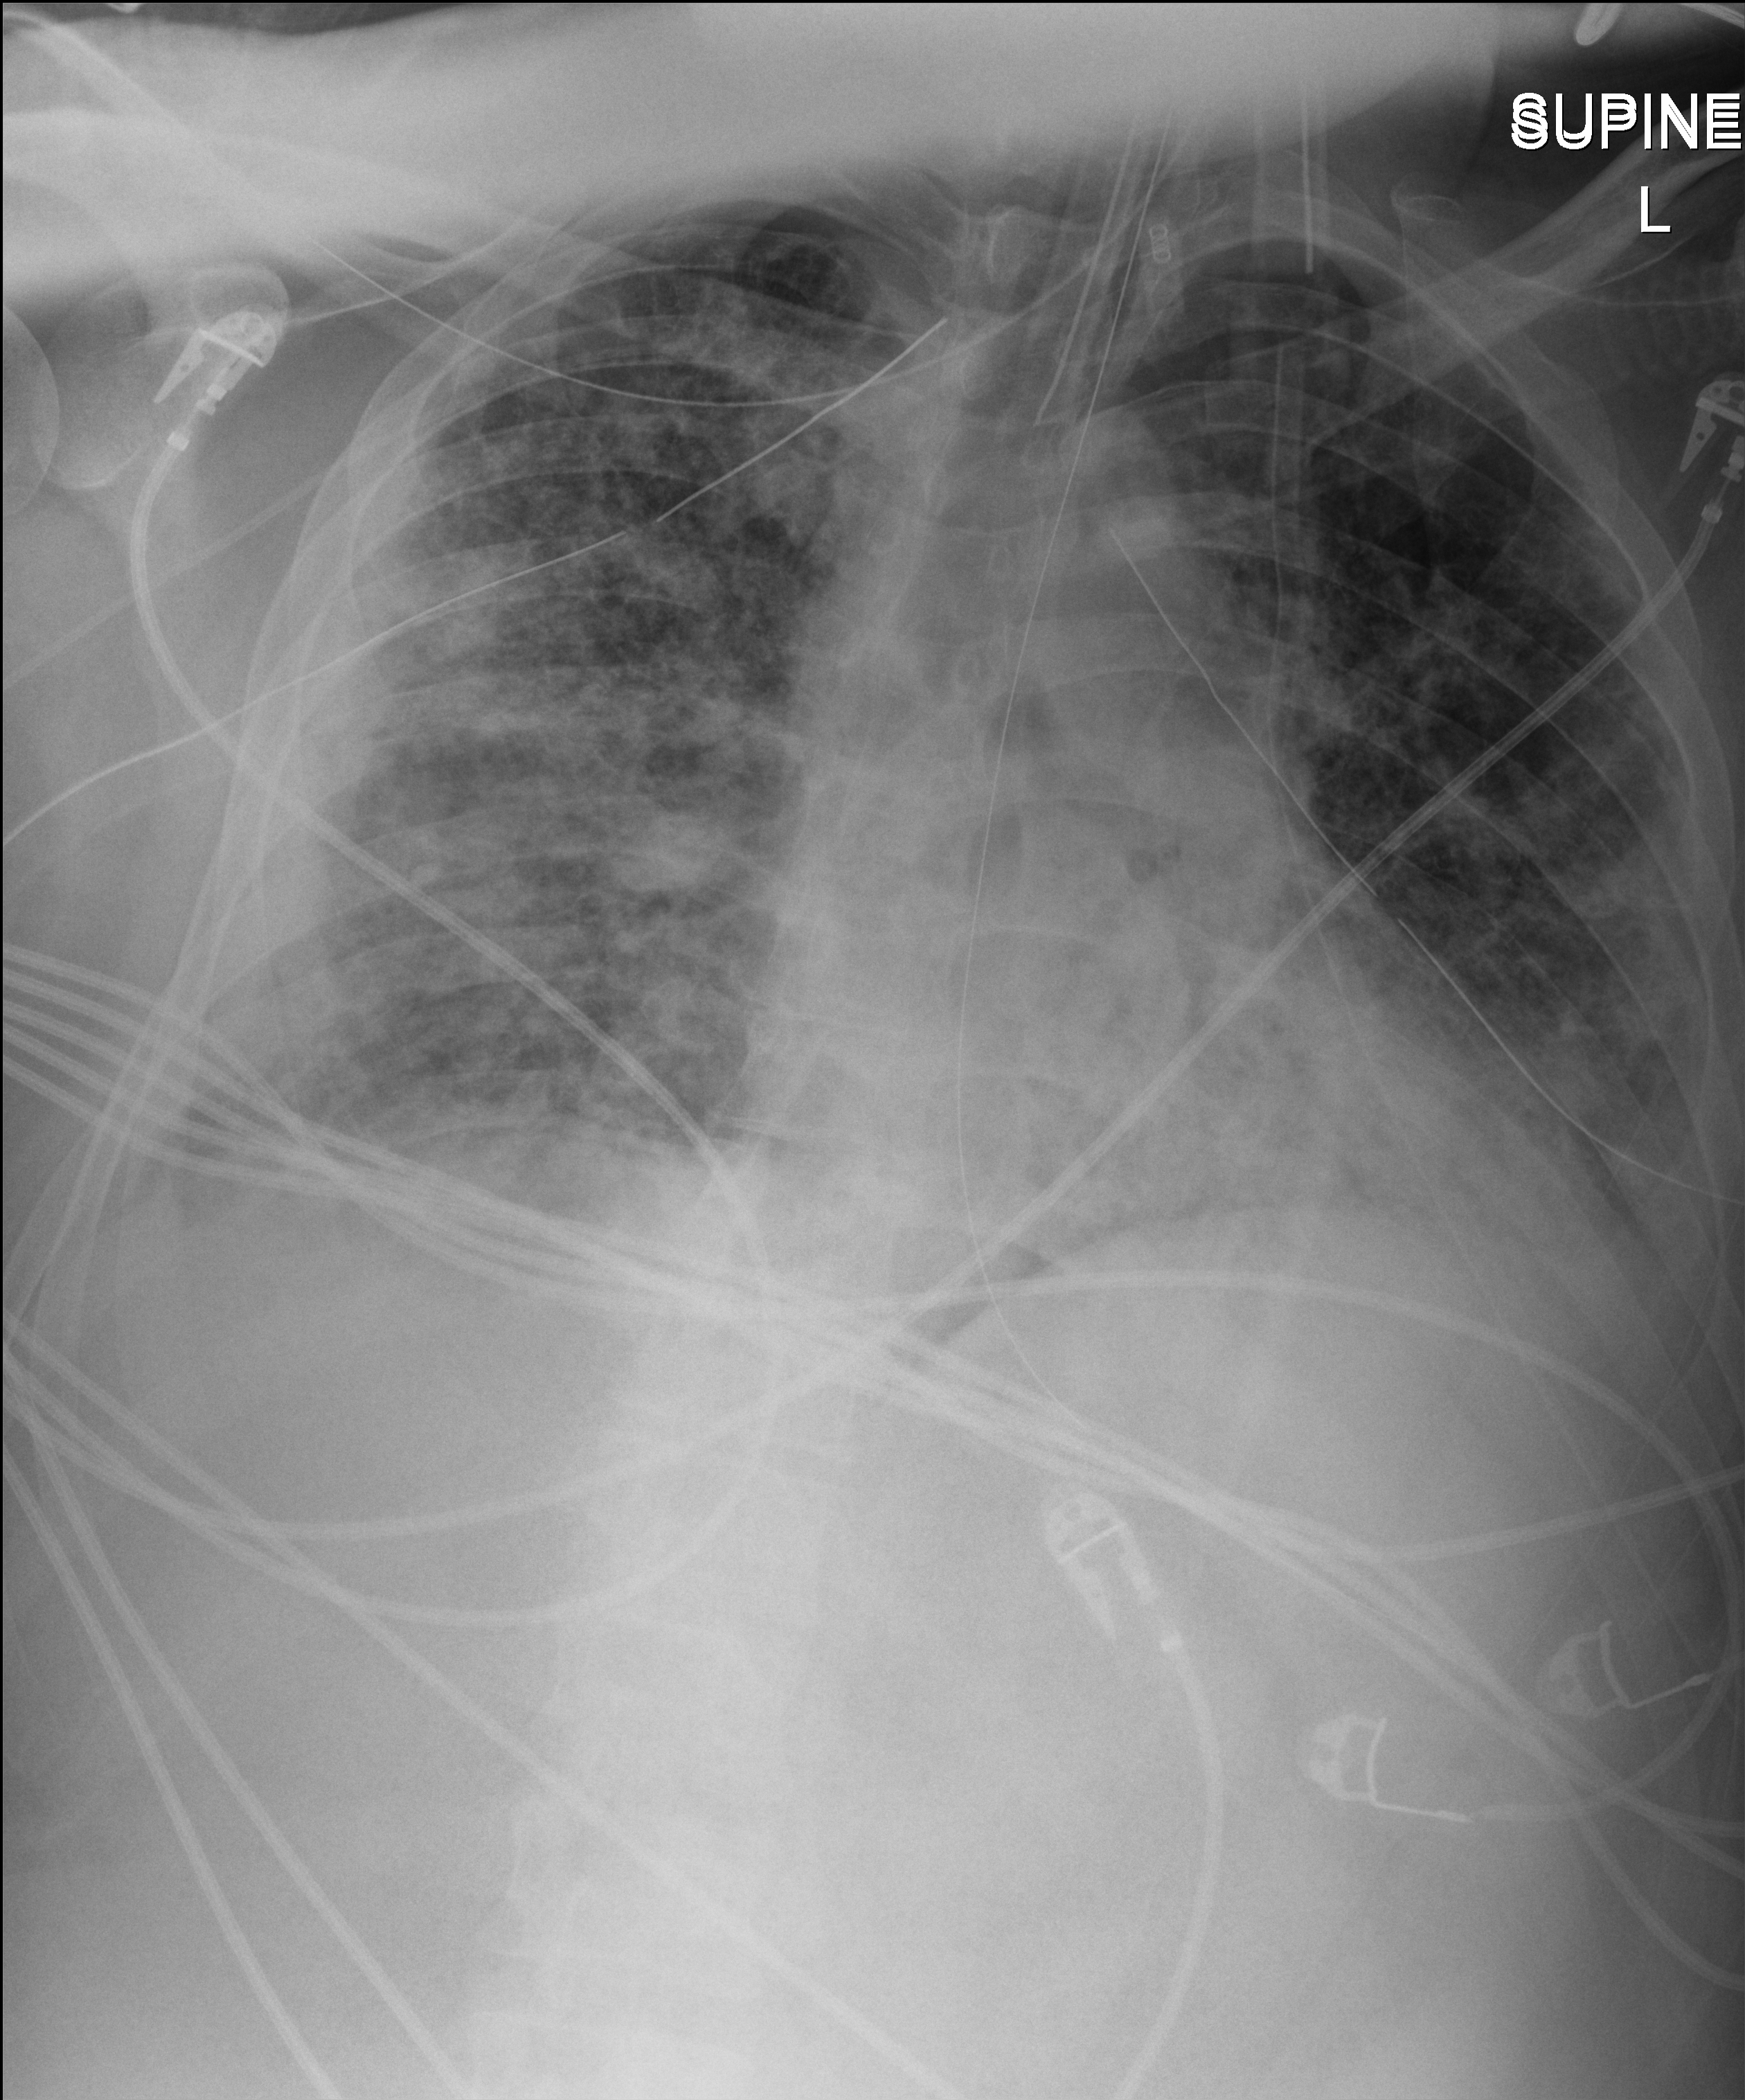
Portable chest radiograph, anteroposterior (AP) projection. Patient hospitalised with COVID-19; male, aged 18–59 years.
Admission-level facts for this patient (not findings on this image; timing relative to this image not recorded):
- mechanically ventilated during this hospital stay: yes